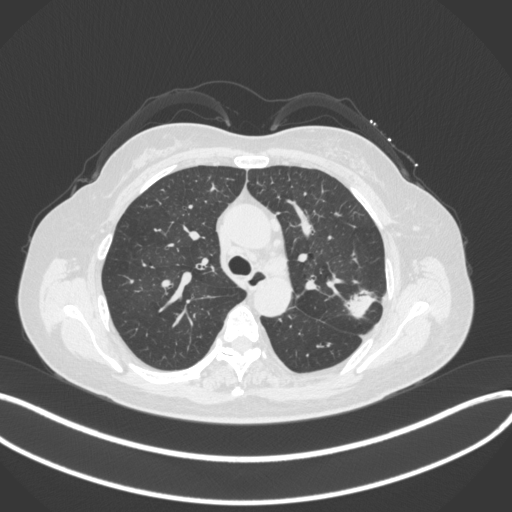
Chest CT, one axial slice; slice 234 of 330 in the series (ordered by position); reconstruction kernel B31f; 120 kVp; lung window (W 1500 / L -600 HU); 512 × 512 image matrix. Patient: female, 60 years. From the clinical record (not read from this slice): clinical TNM (as recorded): T1c N0 M0.
Annotated regions visible in this slice (bounding box drawn by a radiologist):
- lung tumour (recorded histology: adenocarcinoma): bounding box [x1, y1, x2, y2] px = [340, 289, 378, 321]